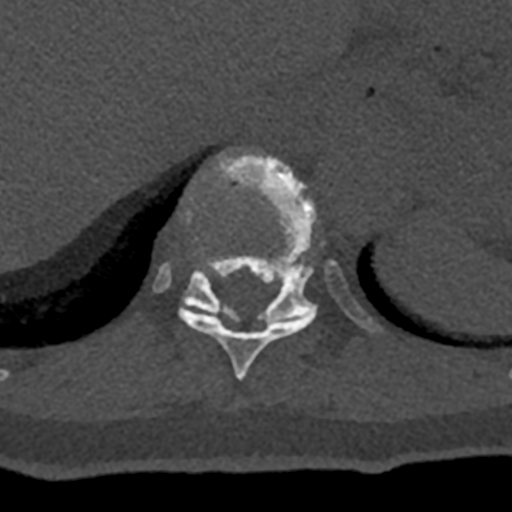
CT including the spine, one axial slice. Slice 581 of 797 in the series (ordered by position). Reconstruction kernel Br40s/3. 120 kVp. Bone window (W 1800 / L 400 HU). 512 × 512 image matrix. Patient: male, 74 years. Case-level facts recorded for this patient, not image findings: primary cancer: renal; vertebrae with lytic lesions (as recorded): T10, L1, L2, L3, L4, L5.
Structures marked on this image (semi-automatic segmentation, software-assisted and operator-edited):
- T10 vertebra: bounding box (x1, y1, x2, y2) in pixels: (178, 152, 316, 380)
- T11 vertebra: (153, 148, 383, 333)